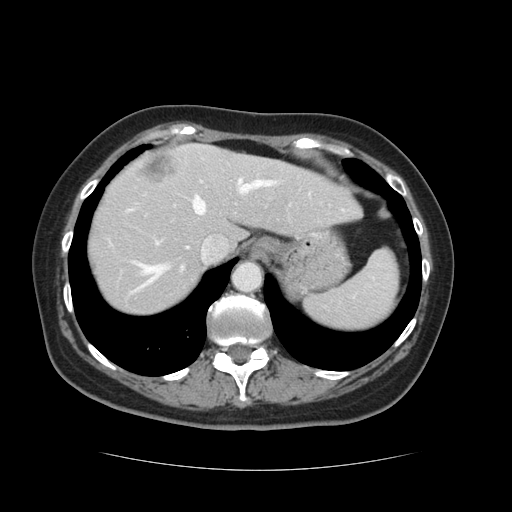
Contrast-enhanced abdominal CT, one axial slice; slice 102 of 128 in the series (ordered by position); 120 kVp; intravenous contrast given; soft-tissue window (W 400 / L 40 HU); 512 × 512 image matrix, field of view 366 × 366 mm. Female patient, age 67 years. From the clinical record (not read from this slice): diagnosis: colorectal cancer liver metastases, imaged before liver resection; multiple liver metastases: yes; largest metastasis: 3 cm; disease in both lobes: yes.
Annotated regions visible in this slice (manually delineated by an expert):
- hepatic veins: bounding box [x1, y1, x2, y2] px = [129, 179, 276, 295]
- liver: [87, 145, 358, 315]
- planned liver remnant (the part of the liver to remain after resection): [87, 155, 357, 316]
- portal vein (with intrahepatic branches): [157, 179, 203, 244]
- liver metastasis: [143, 156, 172, 181]